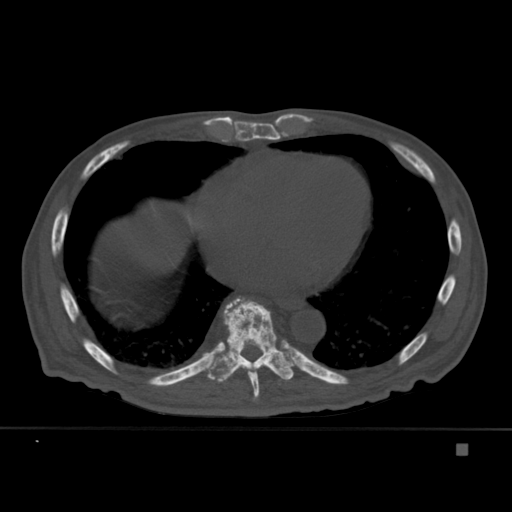
CT including the spine, one axial slice. Bone window (W 1800 / L 400 HU). 1.5 mm slice thickness. 512 × 512 image matrix, field of view 378 × 378 mm. Patient: male, 75 years. From the clinical record (not read from this slice): primary cancer: prostate.
Structures marked on this image (semi-automatic segmentation, software-assisted and operator-edited):
- T8 vertebra: bounding box [x1, y1, x2, y2] px = [227, 338, 260, 401]
- T9 vertebra: [207, 296, 294, 383]